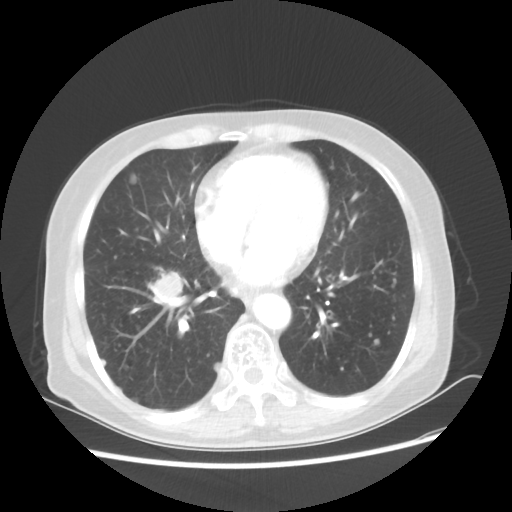
Chest CT, one axial slice; slice 21 of 56 in the series (ordered by position); lung window (W 1500 / L -600 HU); 5 mm slice thickness; 512 × 512 image matrix, field of view 360 × 360 mm. Female patient, age 68 years. From the clinical record (not read from this slice): clinical TNM (as recorded): T1c N3 M0.
Structures marked on this image (bounding box drawn by a radiologist):
- lung tumour (recorded histology: squamous cell carcinoma): bounding box [x1, y1, x2, y2] px = [150, 267, 195, 306]